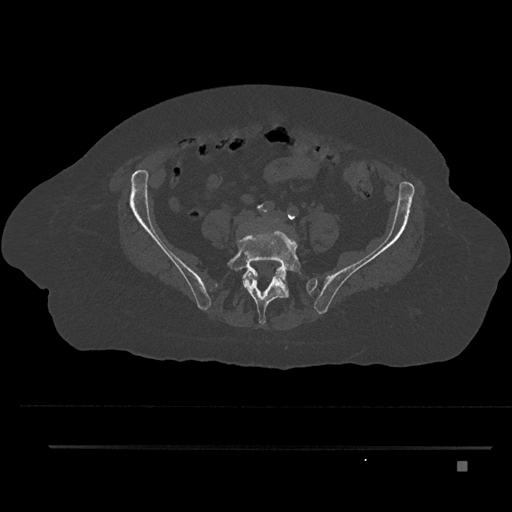
CT including the spine, one axial slice. Slice 41 of 797 in the series (ordered by position). Reconstruction kernel Br40s/3. Bone window (W 1800 / L 400 HU). 0.5 mm slice thickness. 512 × 512 image matrix, field of view 437 × 437 mm. Female patient, age 76 years. Case-level facts recorded for this patient, not image findings: primary cancer: lung.
Structures marked on this image (semi-automatically segmented with operator editing):
- L4 vertebra: box from (x=246, y=221) to (x=287, y=284) px
- L5 vertebra: (x=227, y=227)–(x=301, y=325)